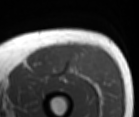
MRI of an extremity soft-tissue mass, one axial slice; position 39 of 86 along the scan axis; MR volume resampled by the dataset authors to the PET/CT grid (not the native acquisition matrix); 3.27 mm slice thickness; 139 × 117 image matrix, field of view 136 × 114 mm. Male patient. Case-level facts recorded for this patient, not image findings: histological type: extraskeletal osteosarcoma; grade: high; site of the primary tumour: thigh.
Annotated regions visible in this slice (expert contour drawn on MRI and transferred to this co-registered scan by the dataset authors):
- gross tumour volume (mass): bounding box (x1, y1, x2, y2) in pixels: (63, 46, 85, 74)